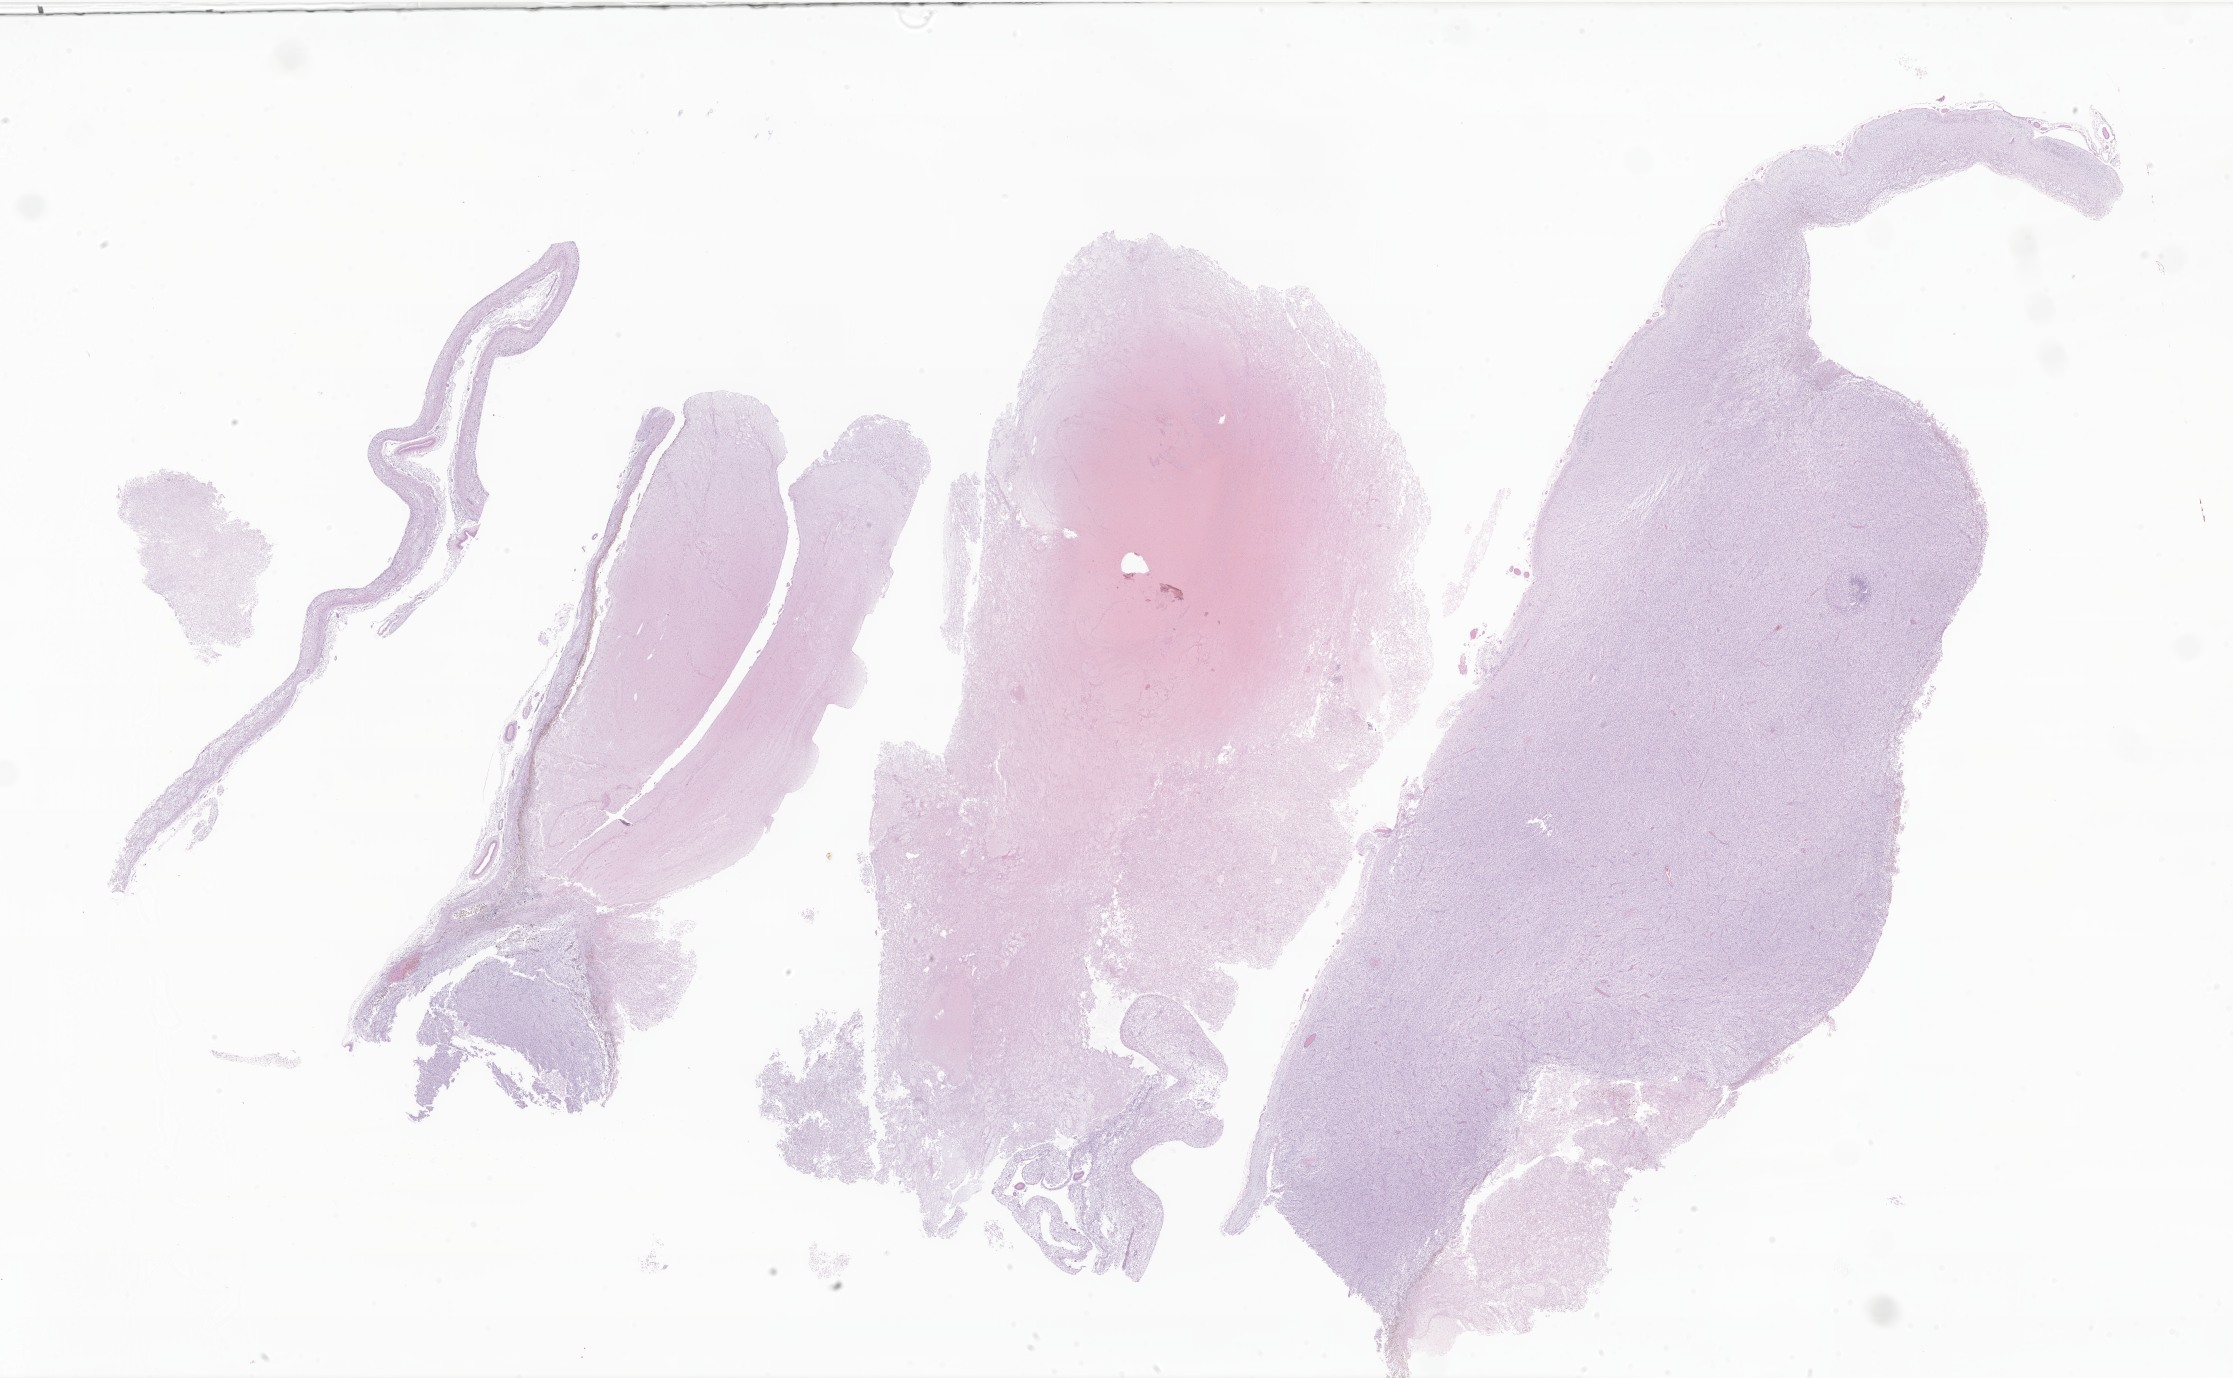
H&E whole-slide image of tumor tissue from the brain, whole scanned area (about 37.7 x 23.2 mm) shown as a low-resolution overview; formalin-fixed paraffin-embedded section. Patient female; age 37 days.
Diagnosis (ICD-O-3 morphology term): Teratoma, NOS.